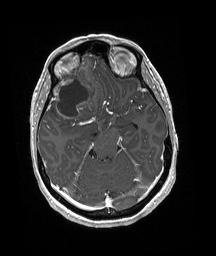
Brain MRI from a brain-tumour surgery series, one axial slice; position 119 of 192 along the scan axis; T1-weighted post-contrast; 216 × 256 image matrix, field of view 211 × 250 mm. Case-level facts recorded for this patient, not image findings: histopathology: Oligodendroglioma; WHO grade: 3.
Annotated regions visible in this slice (outlined manually by an expert reader):
- tumour: bounding box [x1, y1, x2, y2] px = [49, 66, 97, 119]